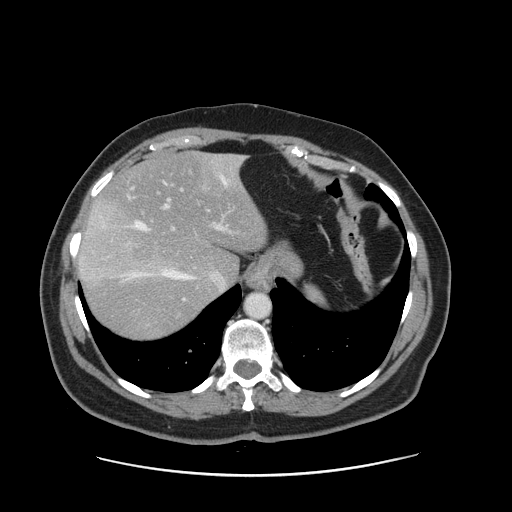
Contrast-enhanced abdominal CT, one axial slice. Position 119 of 161 along the scan axis. Intravenous contrast given. Soft-tissue window (W 400 / L 40 HU). 2.5 mm slice thickness. 512 × 512 image matrix, field of view 398 × 398 mm. Female patient, age 62 years. From the clinical record (not read from this slice): diagnosis: colorectal cancer liver metastases, imaged before liver resection; multiple liver metastases: no; largest metastasis: 2.5 cm.
Structures marked on this image (expert manual segmentation):
- hepatic veins: bounding box (x1, y1, x2, y2) in pixels: (103, 157, 243, 281)
- liver: (79, 153, 267, 340)
- planned liver remnant (the part of the liver to remain after resection): (95, 153, 267, 282)
- portal vein (with intrahepatic branches): (162, 186, 231, 232)